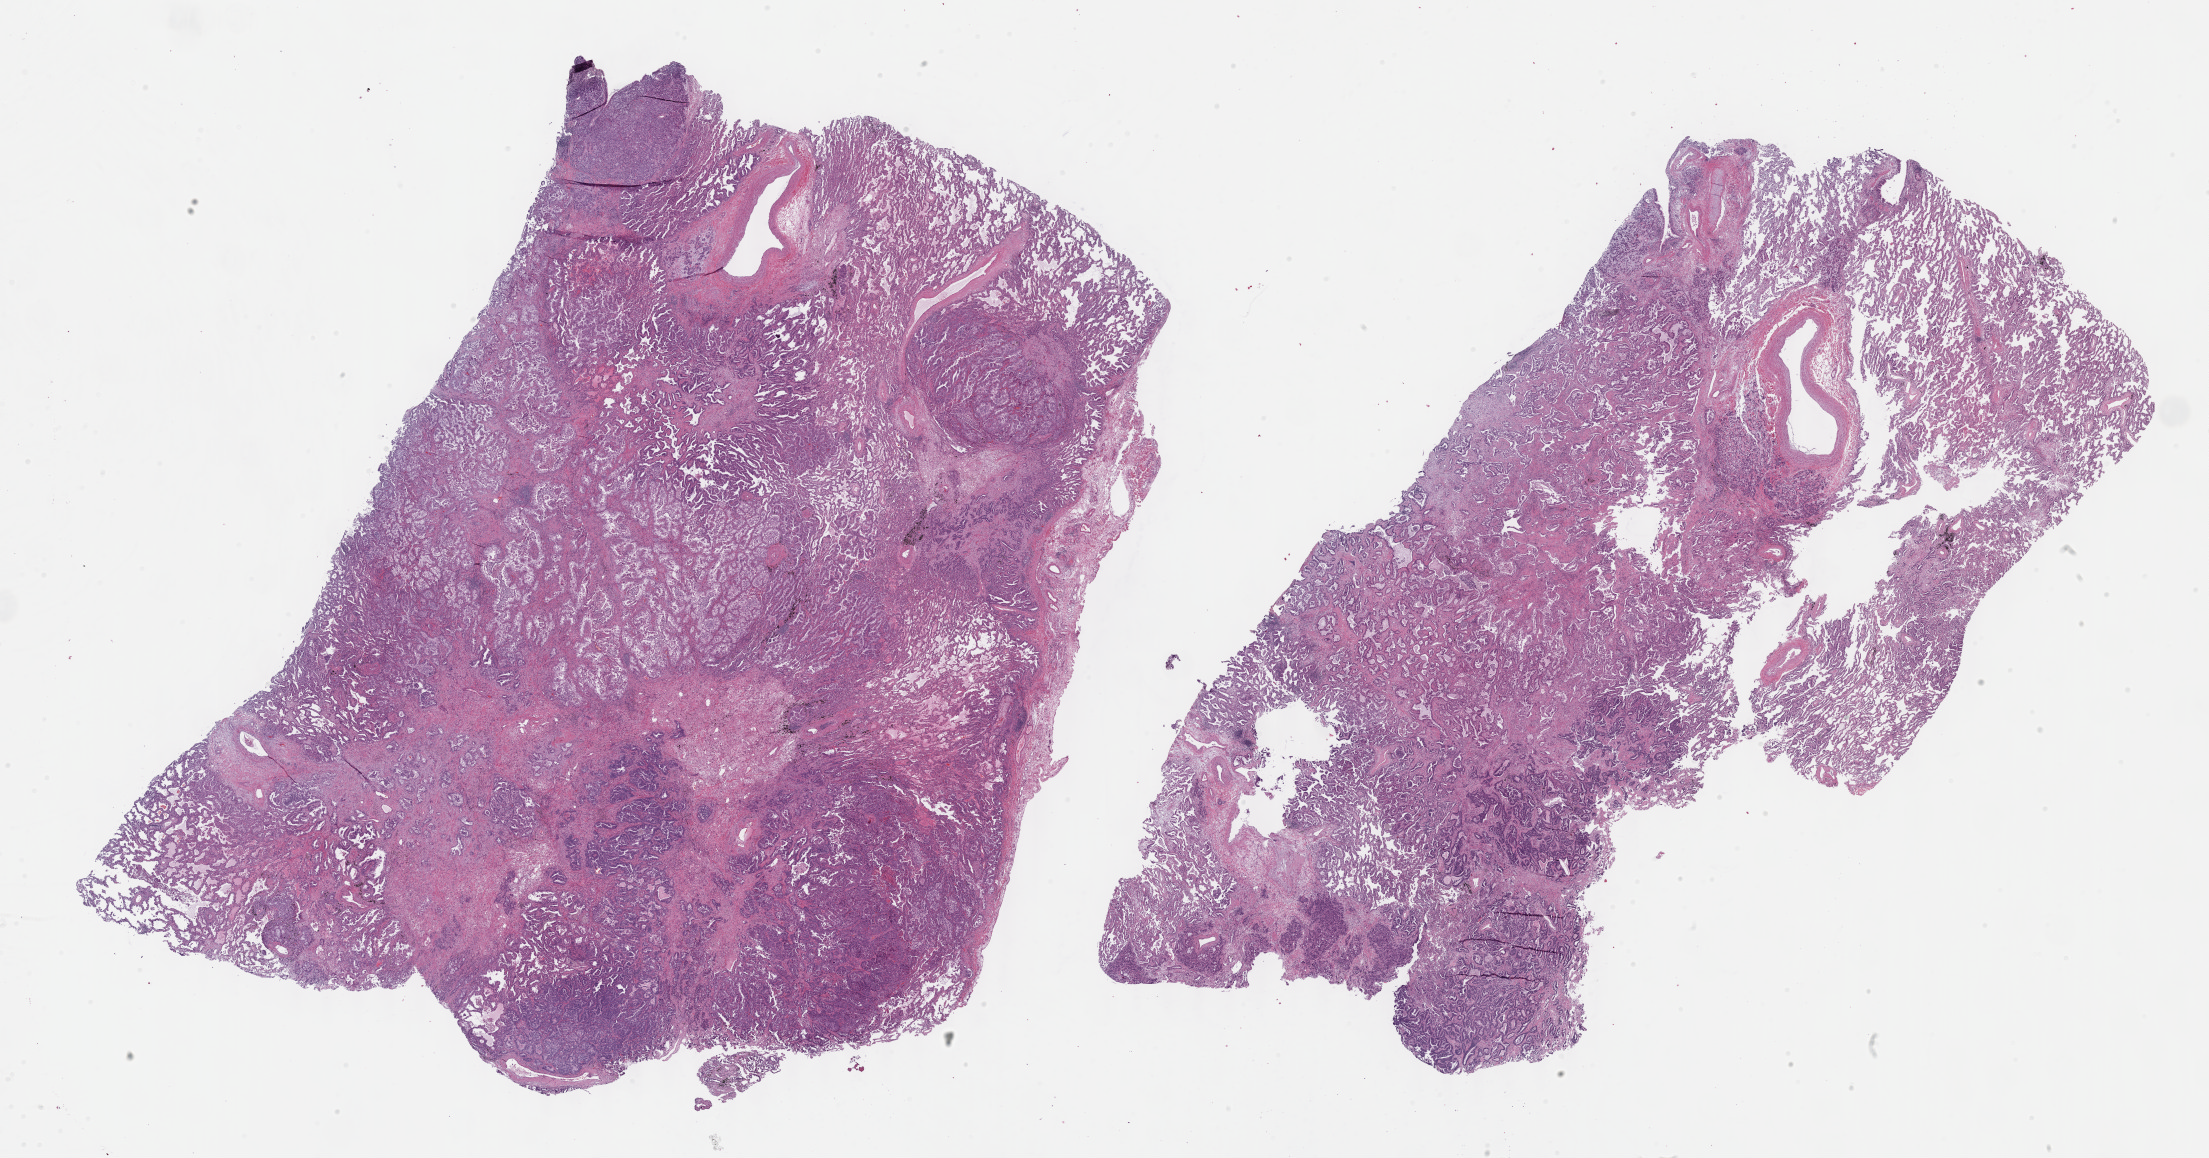
H&E-stained whole-slide image, shown as a low-resolution overview of the whole scanned area (about 35.7 x 18.7 mm, slide scanned at 40x). Formalin-fixed paraffin-embedded (FFPE) diagnostic section. Lung, primary tumour sample. Patient: male, age at initial diagnosis 68 years.
Histologic diagnosis: Adenocarcinoma, NOS (upper lobe, lung).